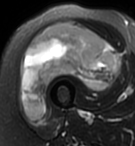
MRI of an extremity soft-tissue mass, one axial slice; slice 41 of 95 in the series (ordered by position); T2-weighted fat-saturated; MR volume resampled by the dataset authors to the PET/CT grid (not the native acquisition matrix); 3.27 mm slice thickness; 135 × 146 image matrix, field of view 132 × 143 mm. Female patient. From the clinical record (not read from this slice): histological type: pleiomorphic undifferentiated sarcoma; grade: high; site of the primary tumour: right quadricep.
Annotated regions visible in this slice (expert contour drawn on MRI and transferred to this co-registered scan by the dataset authors):
- gross tumour volume including surrounding oedema: box from (x=21, y=24) to (x=120, y=119) px
- gross tumour volume (mass): (x=21, y=24)–(x=120, y=119)